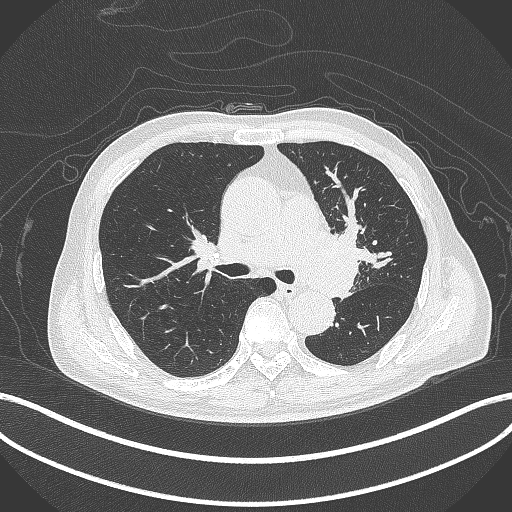
Chest CT, one axial slice. Slice 267 of 417 in the series (ordered by position). 120 kVp. Lung window (W 1500 / L -600 HU). 1 mm slice thickness. 512 × 512 image matrix, field of view 400 × 400 mm. Patient: male, 77 years. Case-level facts recorded for this patient, not image findings: clinical TNM (as recorded): T3 N1 M0.
Outlined on this slice (rectangle marked by the reading radiologist):
- lung tumour (recorded histology: adenocarcinoma): bounding box <313,222,363,297> (left, top, right, bottom; pixels)